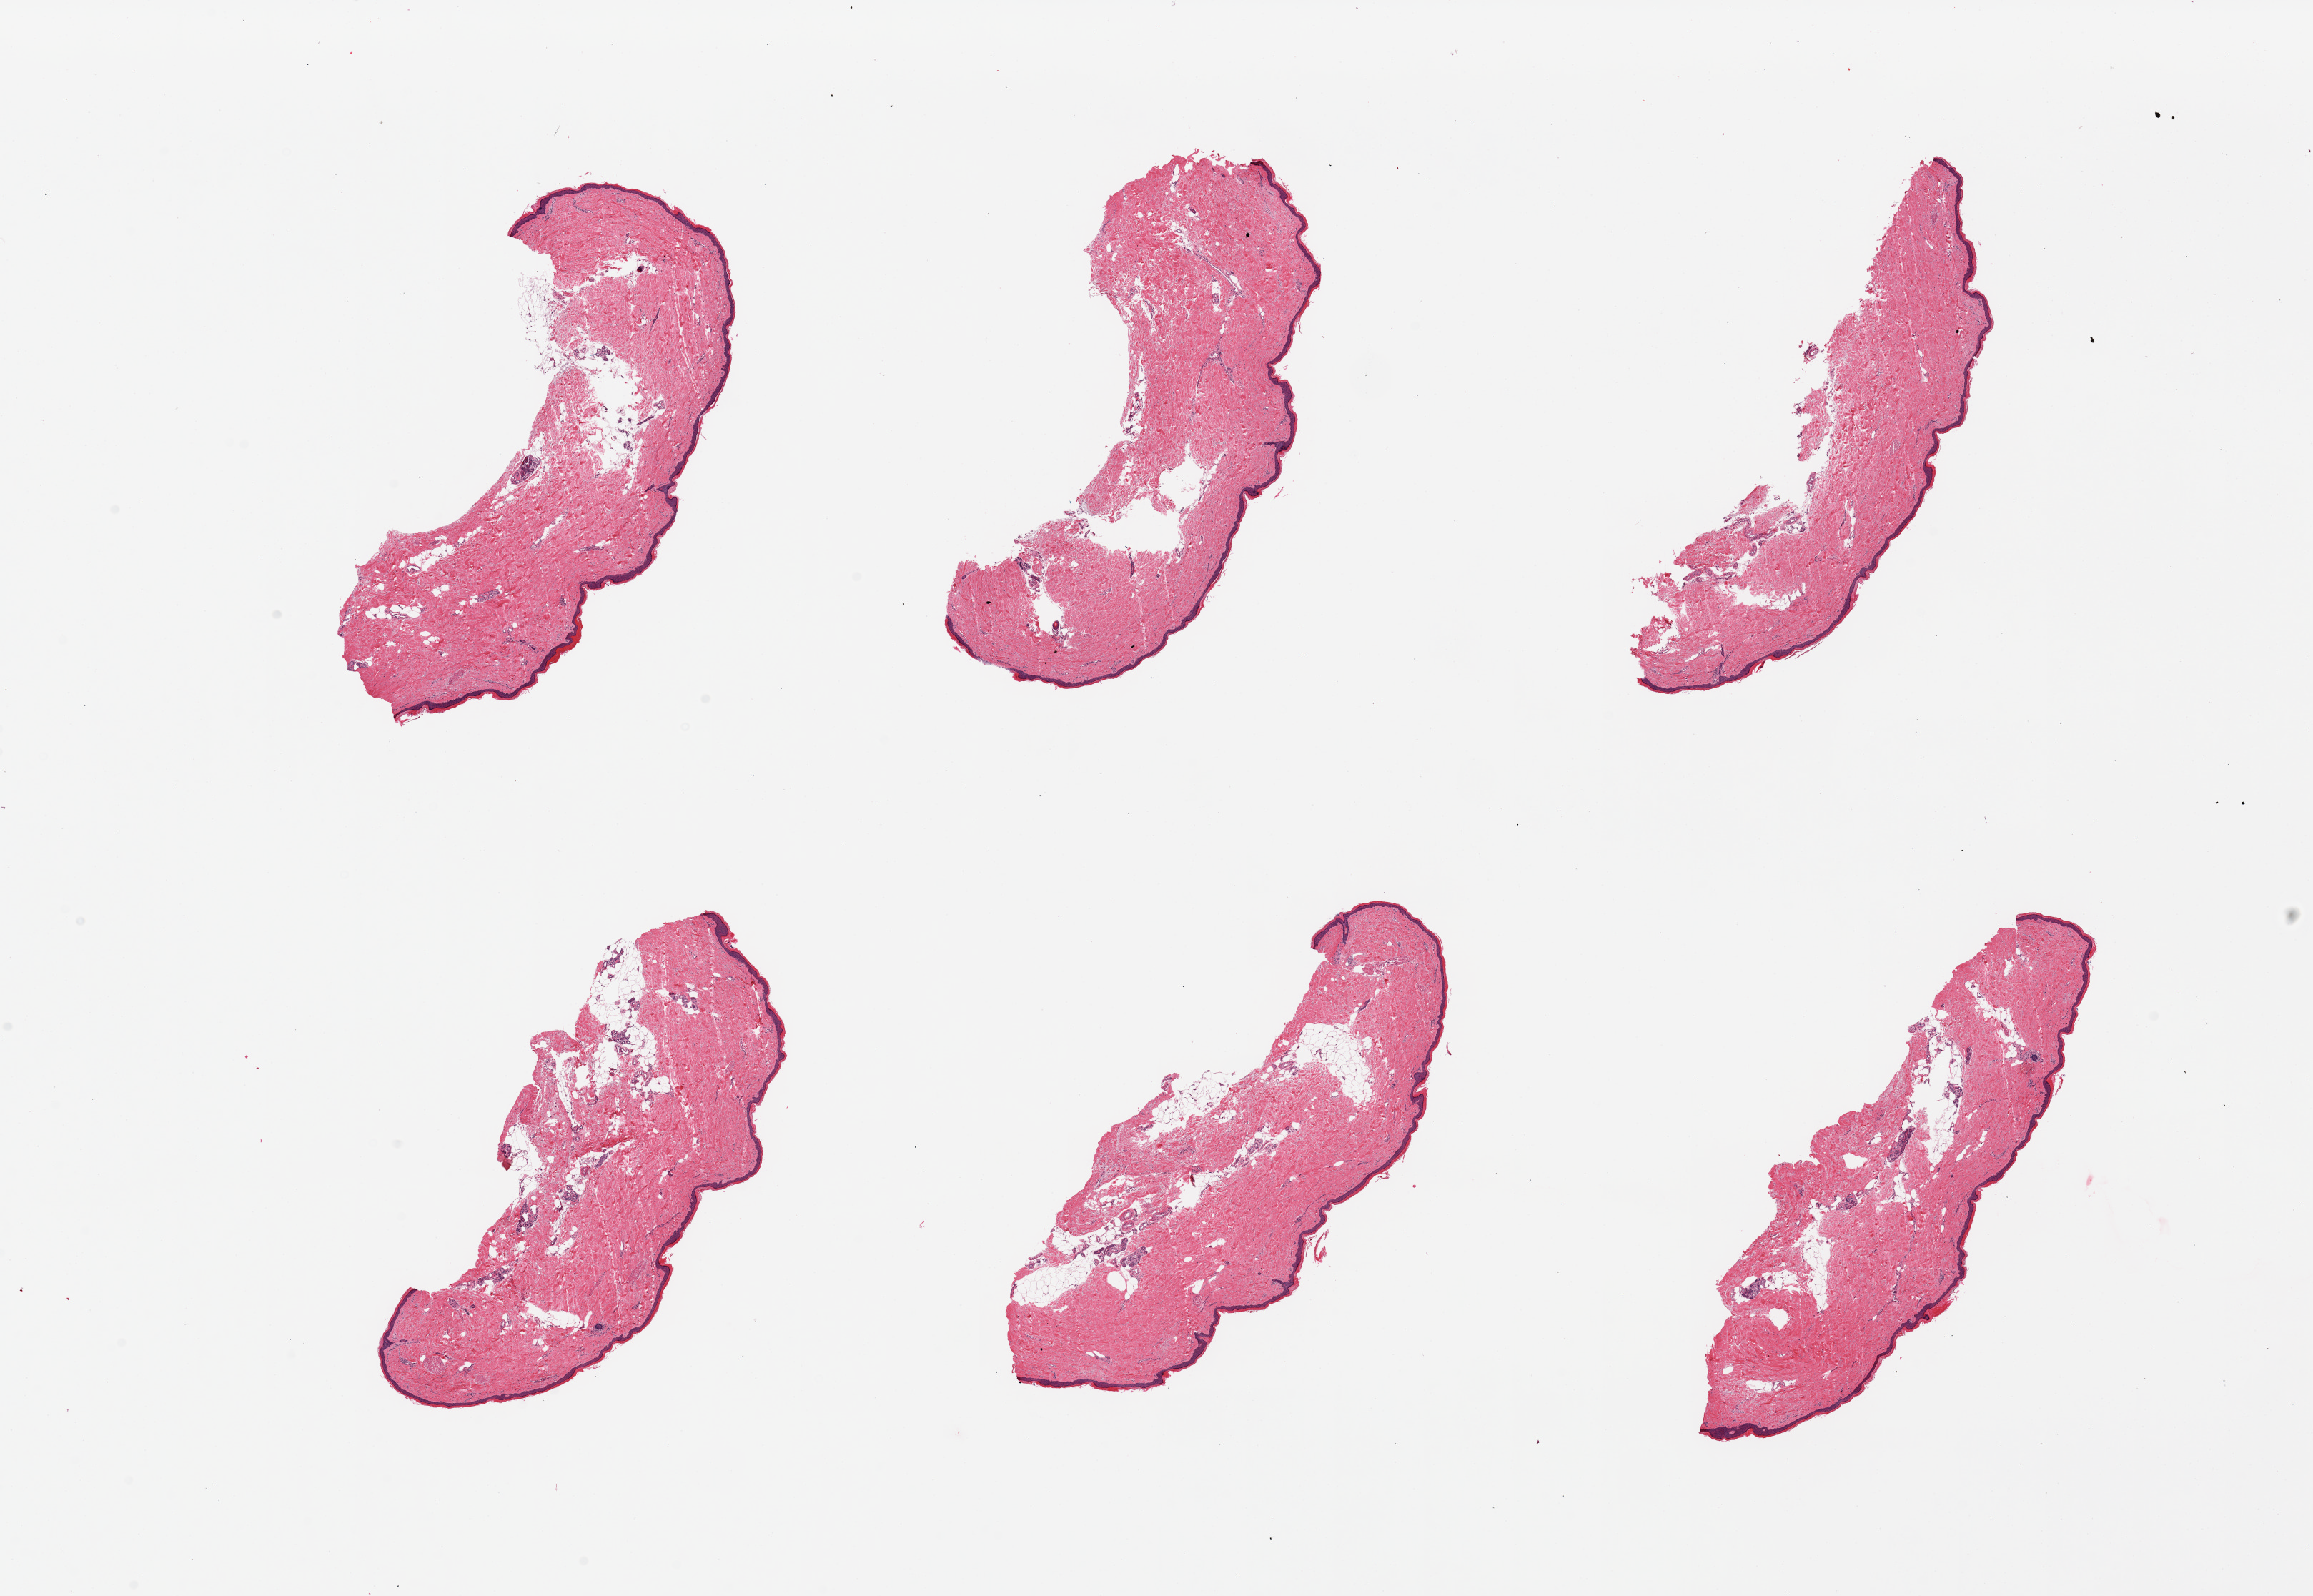
Digitized haematoxylin and eosin-stained section, whole scanned area (about 25.6 x 17.7 mm, from a 20x scan) shown as a low-resolution overview, PAXgene-fixed paraffin-embedded (PFPE) section, sampled site (target tissue): skin of lower leg, donor tissue sample.
Review note (as recorded): 6 pieces, squamous epithelium is ~10microns thick, 1-2 % total thickness.